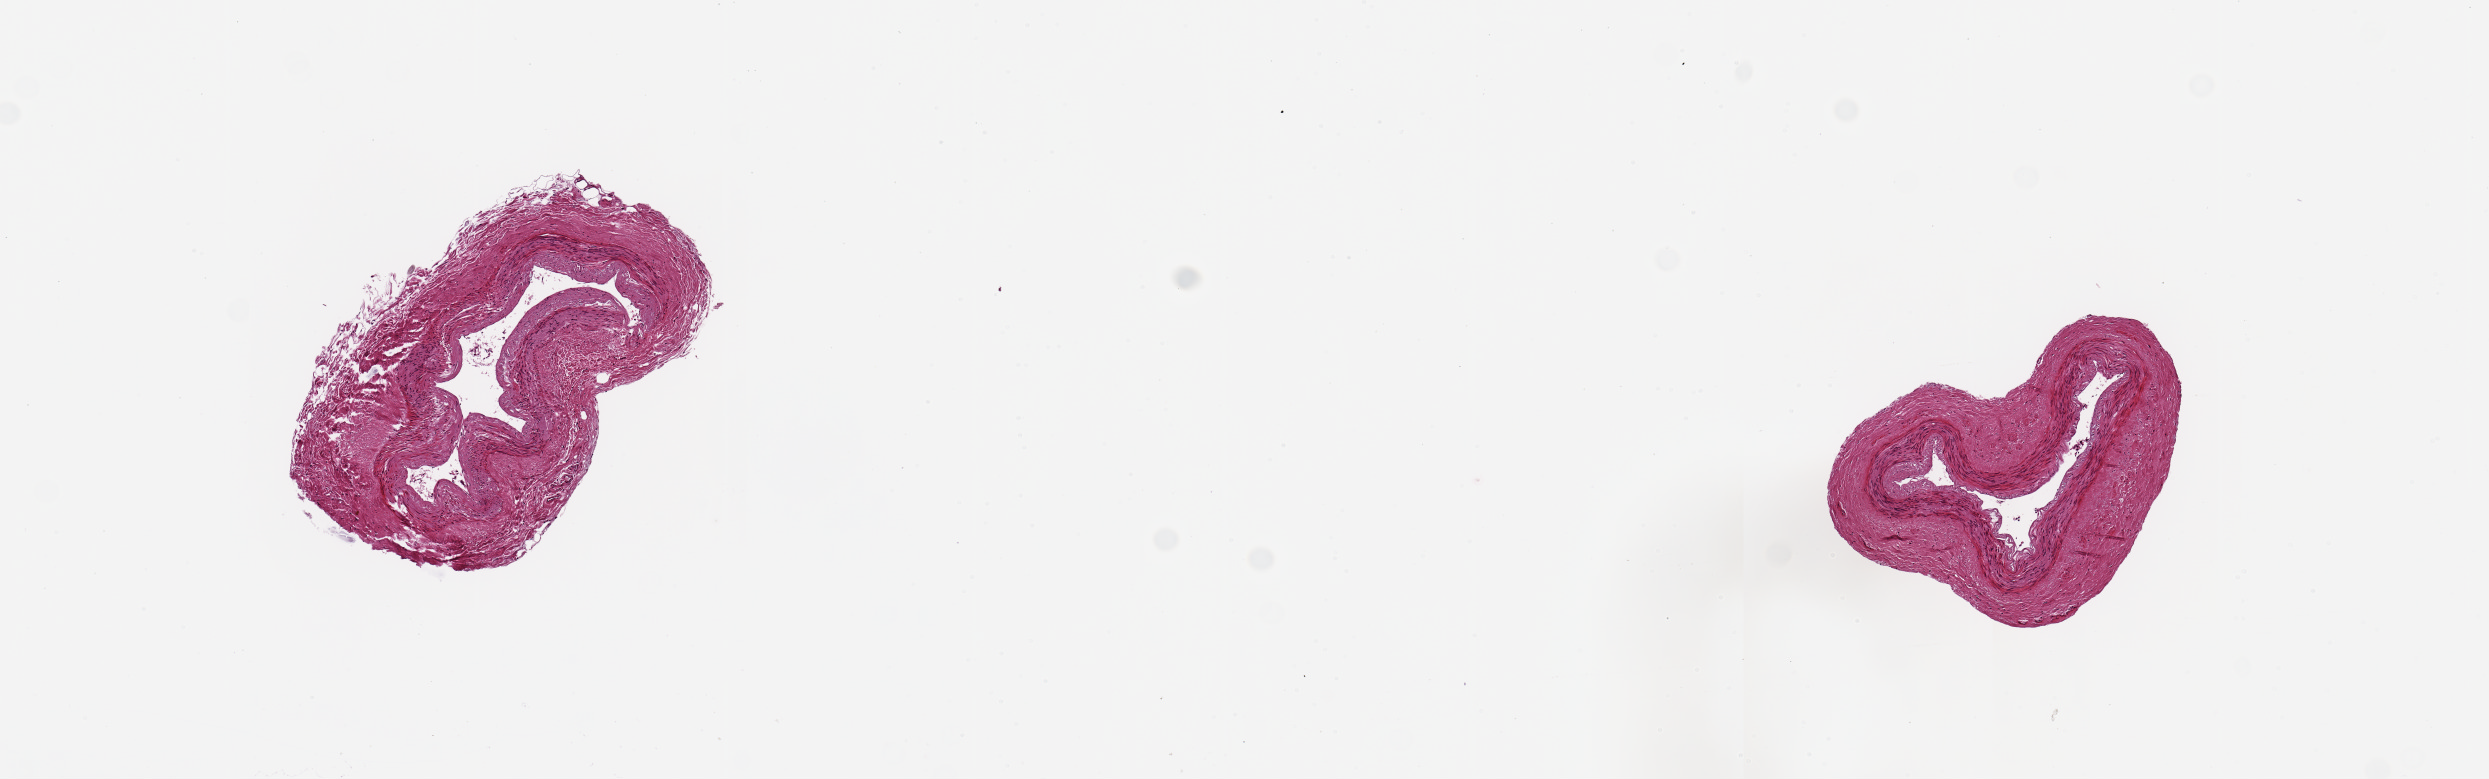
Digitized haematoxylin and eosin-stained section, shown as a low-resolution overview of the whole scanned area (about 9.8 x 3.1 mm); PAXgene-fixed paraffin-embedded (PFPE) section; section of tibial artery (target tissue); tissue donor sample. Donor sex: female.
Review note (as recorded): 2 ~1.3x 0.8mm aliquots; good clean small muscular artery specimens.